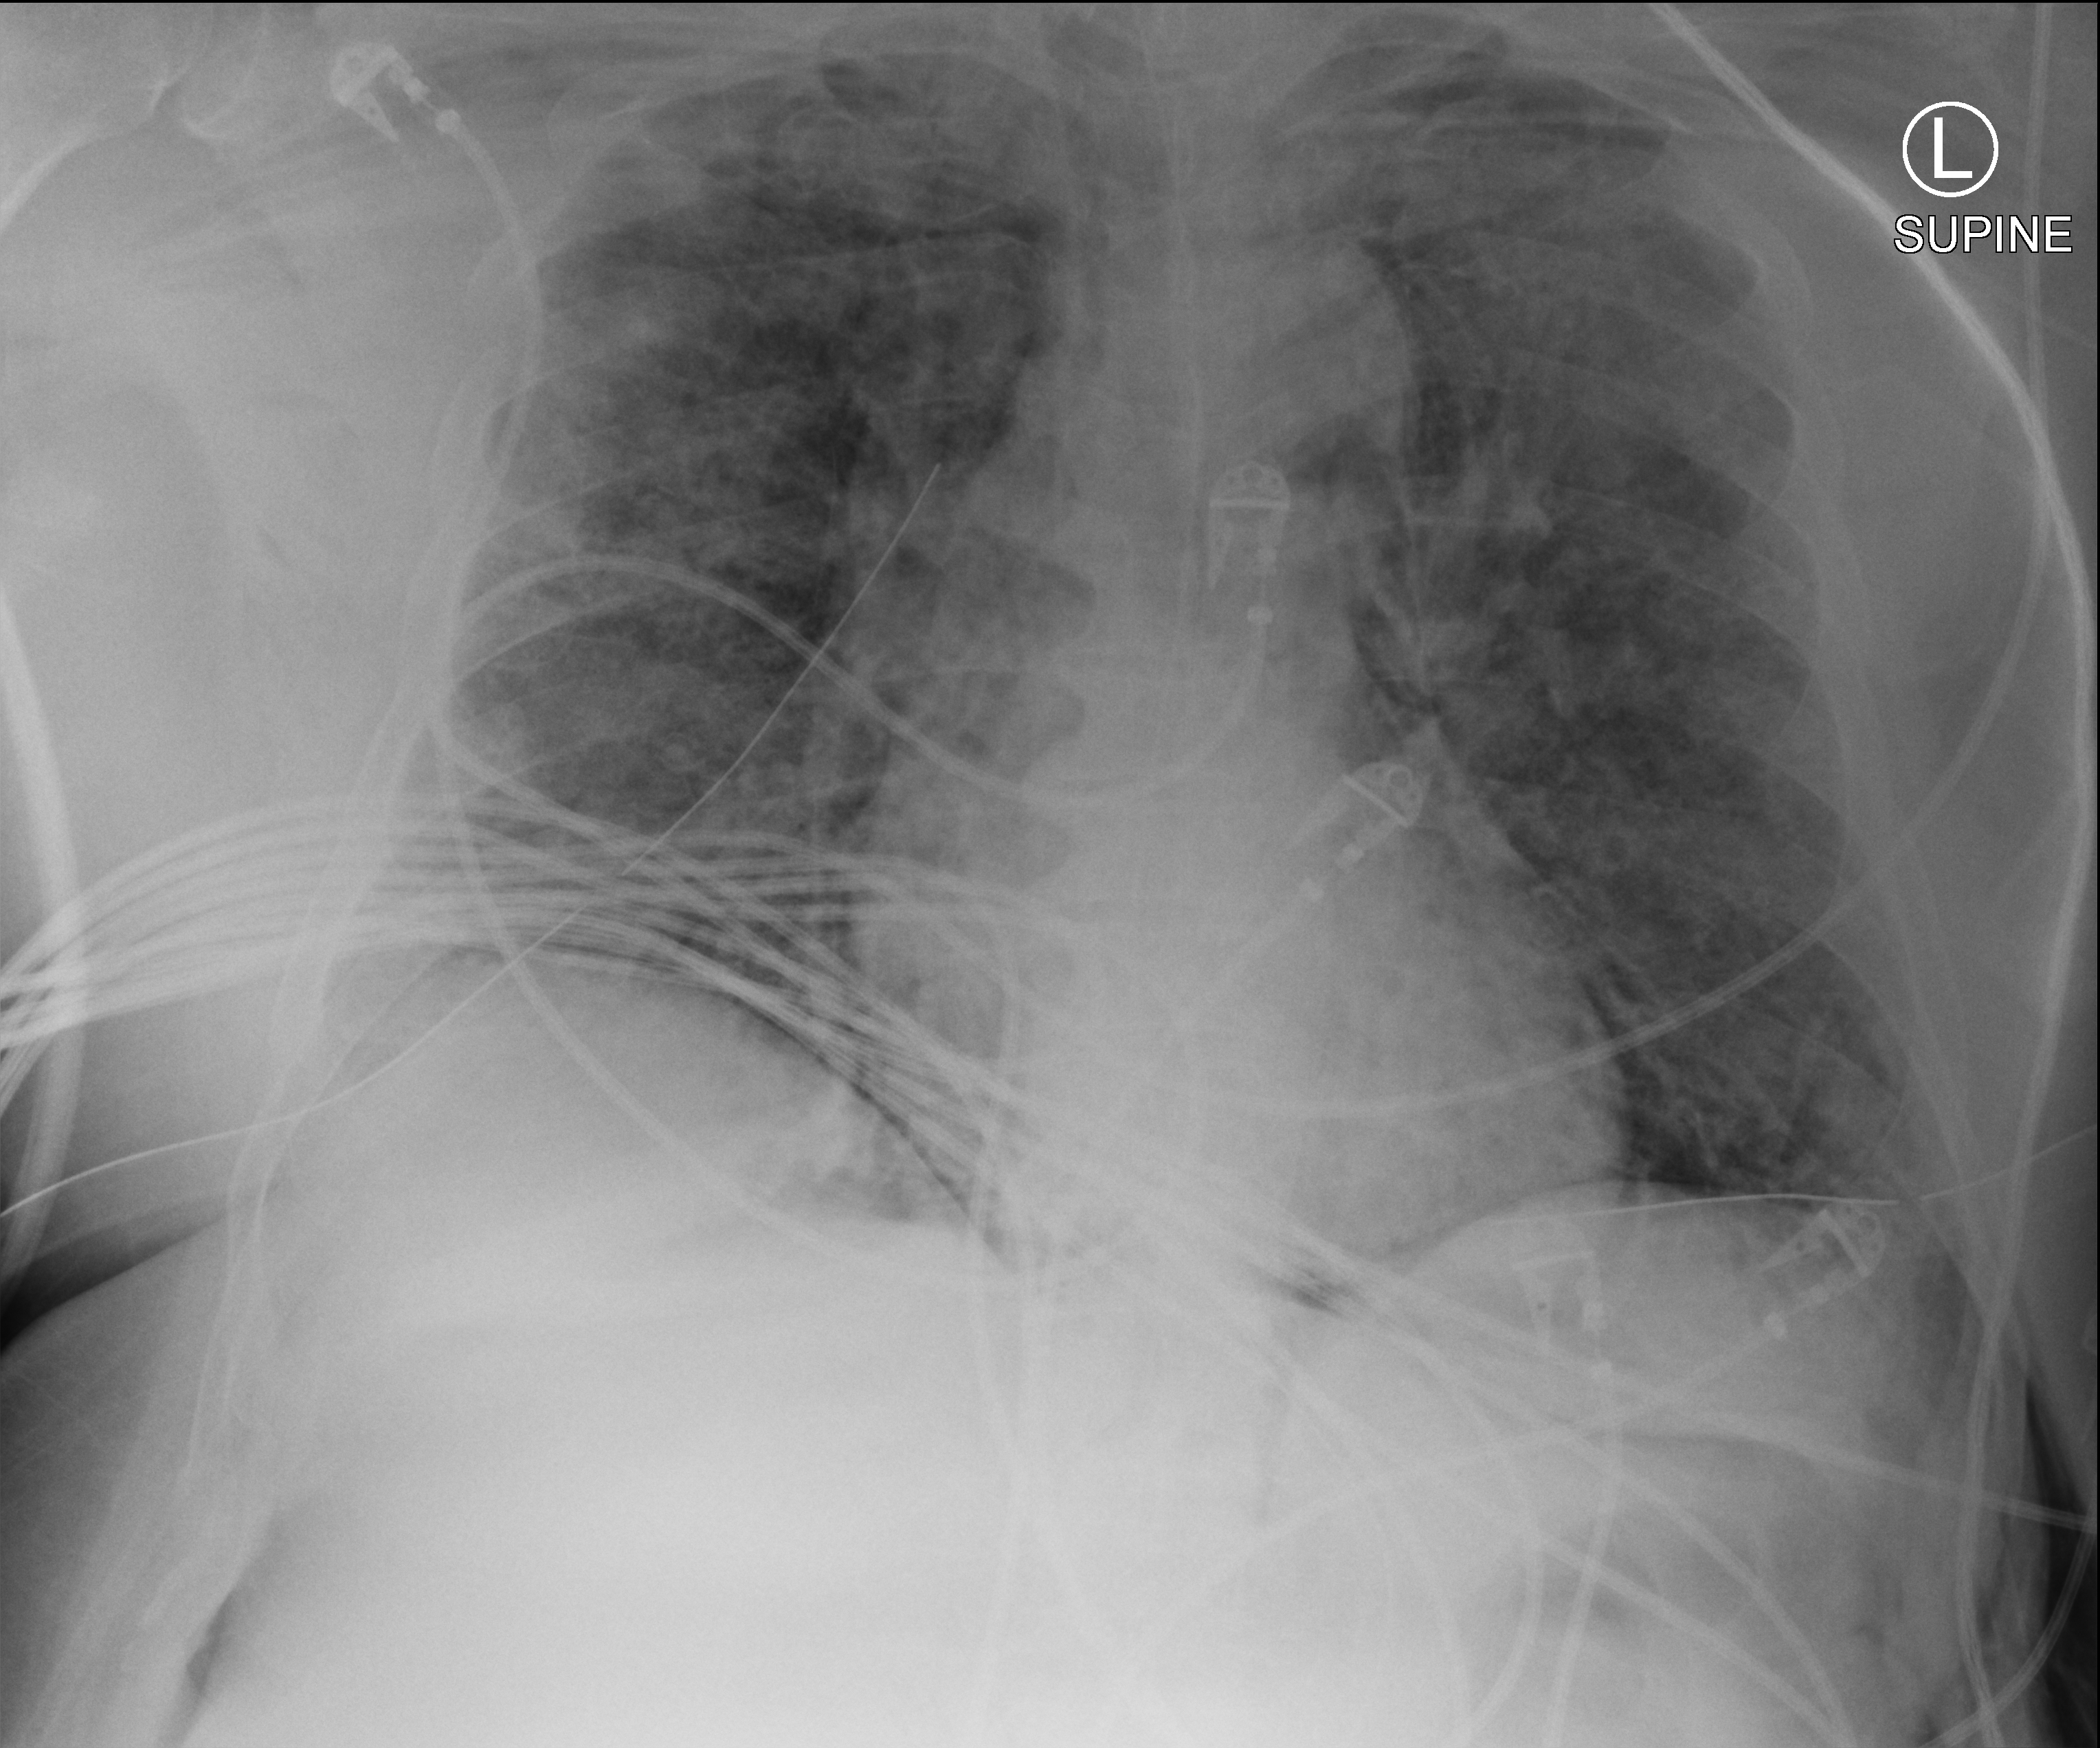
Chest X-ray (portable). Patient hospitalised with COVID-19, aged 18–59 years.
From the hospital-stay record, not from the radiograph (when in the stay this image was taken is not recorded):
- admitted to intensive care during this hospital stay: yes
- length of hospital stay: 28 days
- mechanically ventilated during this hospital stay: yes